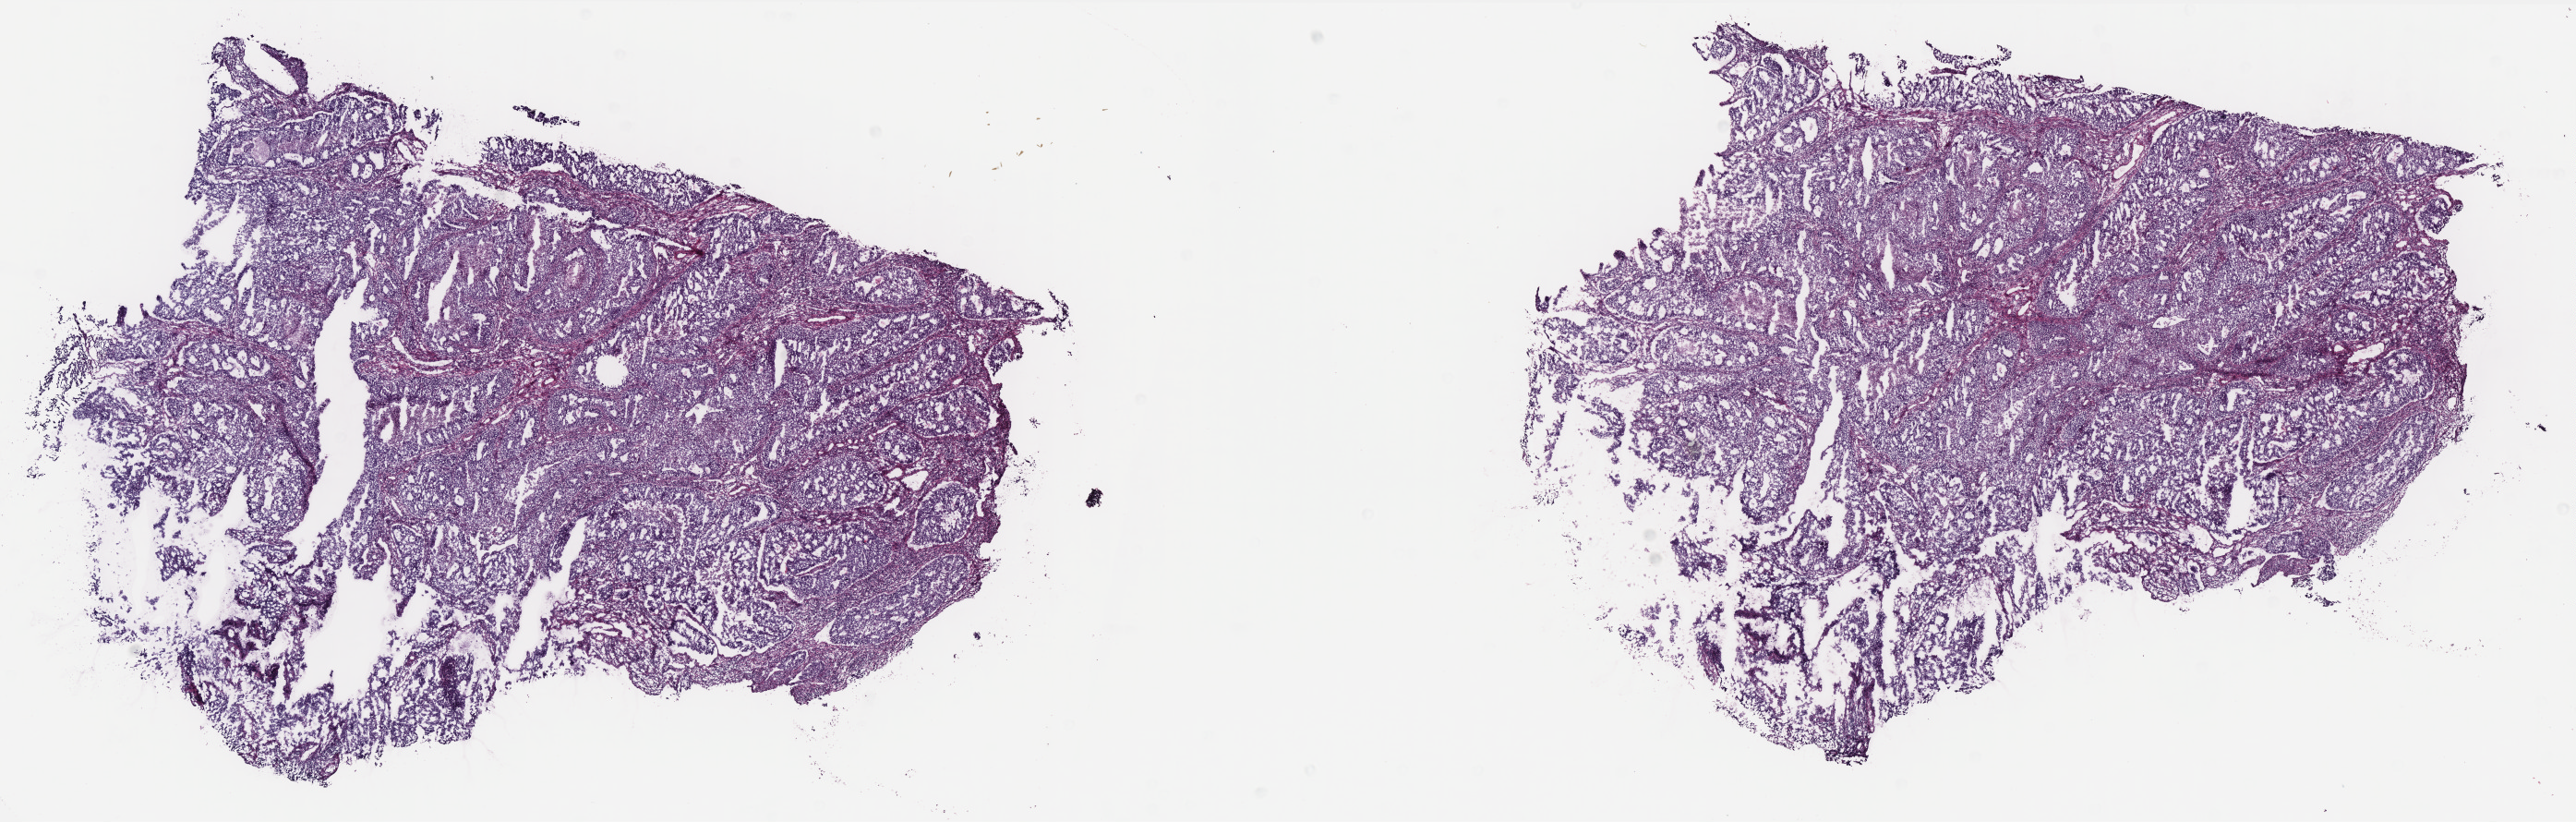
Digitized H&E-stained tissue section (whole slide) — a low-resolution overview of the entire scanned area, about 22.4 x 7.1 mm (acquisition: 40x scan); frozen section from the top of the tissue portion; primary tumour sample from the uterus. Female patient; age at initial diagnosis 38 years. Histologic grade: G2 (moderately differentiated). Pathologist review of this section (percent, as recorded): tumour cells 80%, tumour nuclei 85%, normal cells 10%, stromal cells 5%, necrosis 5%. Inflammatory infiltration, as recorded: lymphocyte infiltration 60%, monocyte infiltration 0%, neutrophil infiltration 30%.
FIGO stage: IA. Pathologic diagnosis: Endometrioid adenocarcinoma, NOS (endometrium).